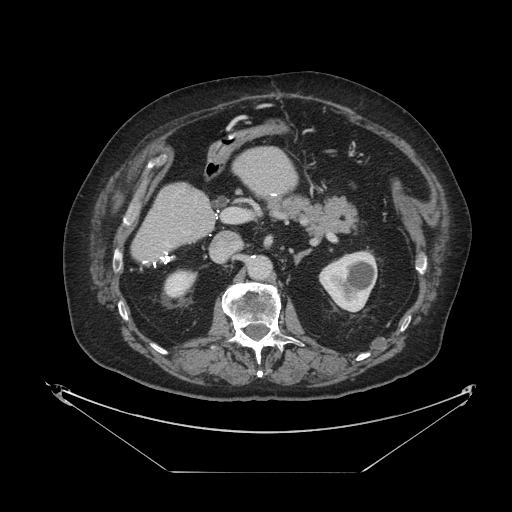
Contrast-enhanced abdominal CT, one axial slice. Slice 46 of 121 in the series (ordered by position). Reconstruction kernel STANDARD. Intravenous contrast given. Soft-tissue window (W 400 / L 40 HU). 512 × 512 image matrix, field of view 500 × 500 mm. Male patient, age 68 years. From the clinical record (not read from this slice): diagnosis: colorectal cancer liver metastases, imaged before liver resection; multiple liver metastases: no; largest metastasis: 4 cm.
Outlined on this slice (outlined manually by an expert reader):
- liver: bounding box <132,148,297,264> (left, top, right, bottom; pixels)
- planned liver remnant (the part of the liver to remain after resection): <132,148,297,264>
- portal vein (with intrahepatic branches): <223,208,237,222>